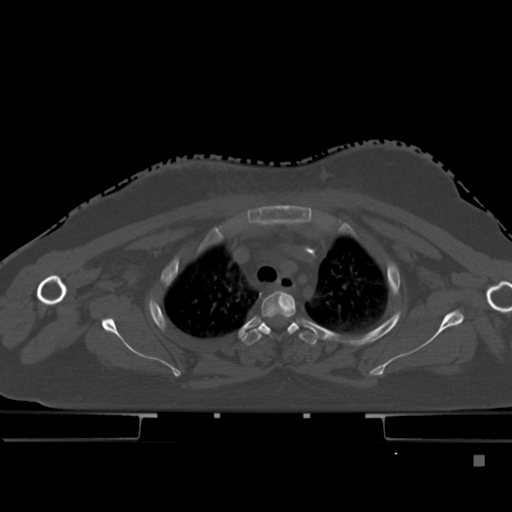
CT including the spine, one axial slice; slice 352 of 495 in the series (ordered by position); bone window (W 1800 / L 400 HU); 1.5 mm slice thickness; 512 × 512 image matrix, field of view 404 × 404 mm. Female patient, age 33 years. From the clinical record (not read from this slice): primary cancer: breast; vertebrae with lytic lesions (as recorded): T1.
Outlined on this slice (semi-automatically segmented with operator editing):
- T2 vertebra: bounding box [x1, y1, x2, y2] px = [261, 291, 296, 335]
- T3 vertebra: [240, 321, 318, 345]